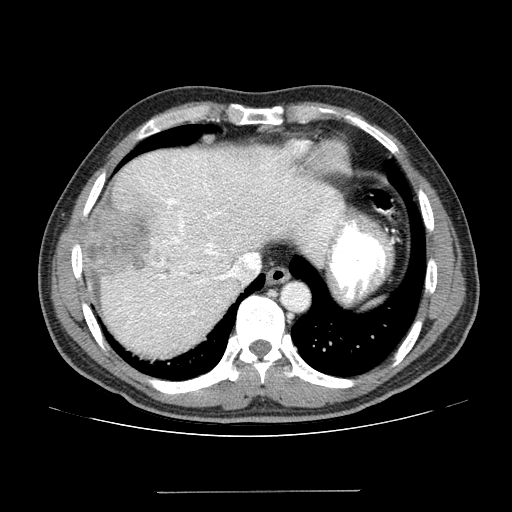
Contrast-enhanced abdominal CT (liver protocol), one axial slice; position 111 of 131 along the scan axis; one of 2 acquisitions stored at this slice position; soft-tissue window (W 400 / L 40 HU); 2.5 mm slice thickness; 512 × 512 image matrix, field of view 380 × 380 mm. Case-level facts recorded for this patient, not image findings: diagnosis: hepatocellular carcinoma (patient treated with transarterial chemoembolisation; whether this scan precedes or follows treatment is not stated here); TNM stage (as recorded): Stage-I; Child-Pugh class: A; tumour differentiation: poorly differentiated; tumour nodularity: uninodular.
Annotated regions visible in this slice (semi-automatically segmented with operator editing):
- abdominal aorta: bounding box (x1, y1, x2, y2) in pixels: (282, 284, 308, 310)
- liver parenchyma outside the tumour (the mass and vessels are separate outlines, so this box may not span the whole liver): (82, 146, 344, 358)
- mass: (82, 207, 159, 280)
- liver vessels: (116, 155, 343, 328)